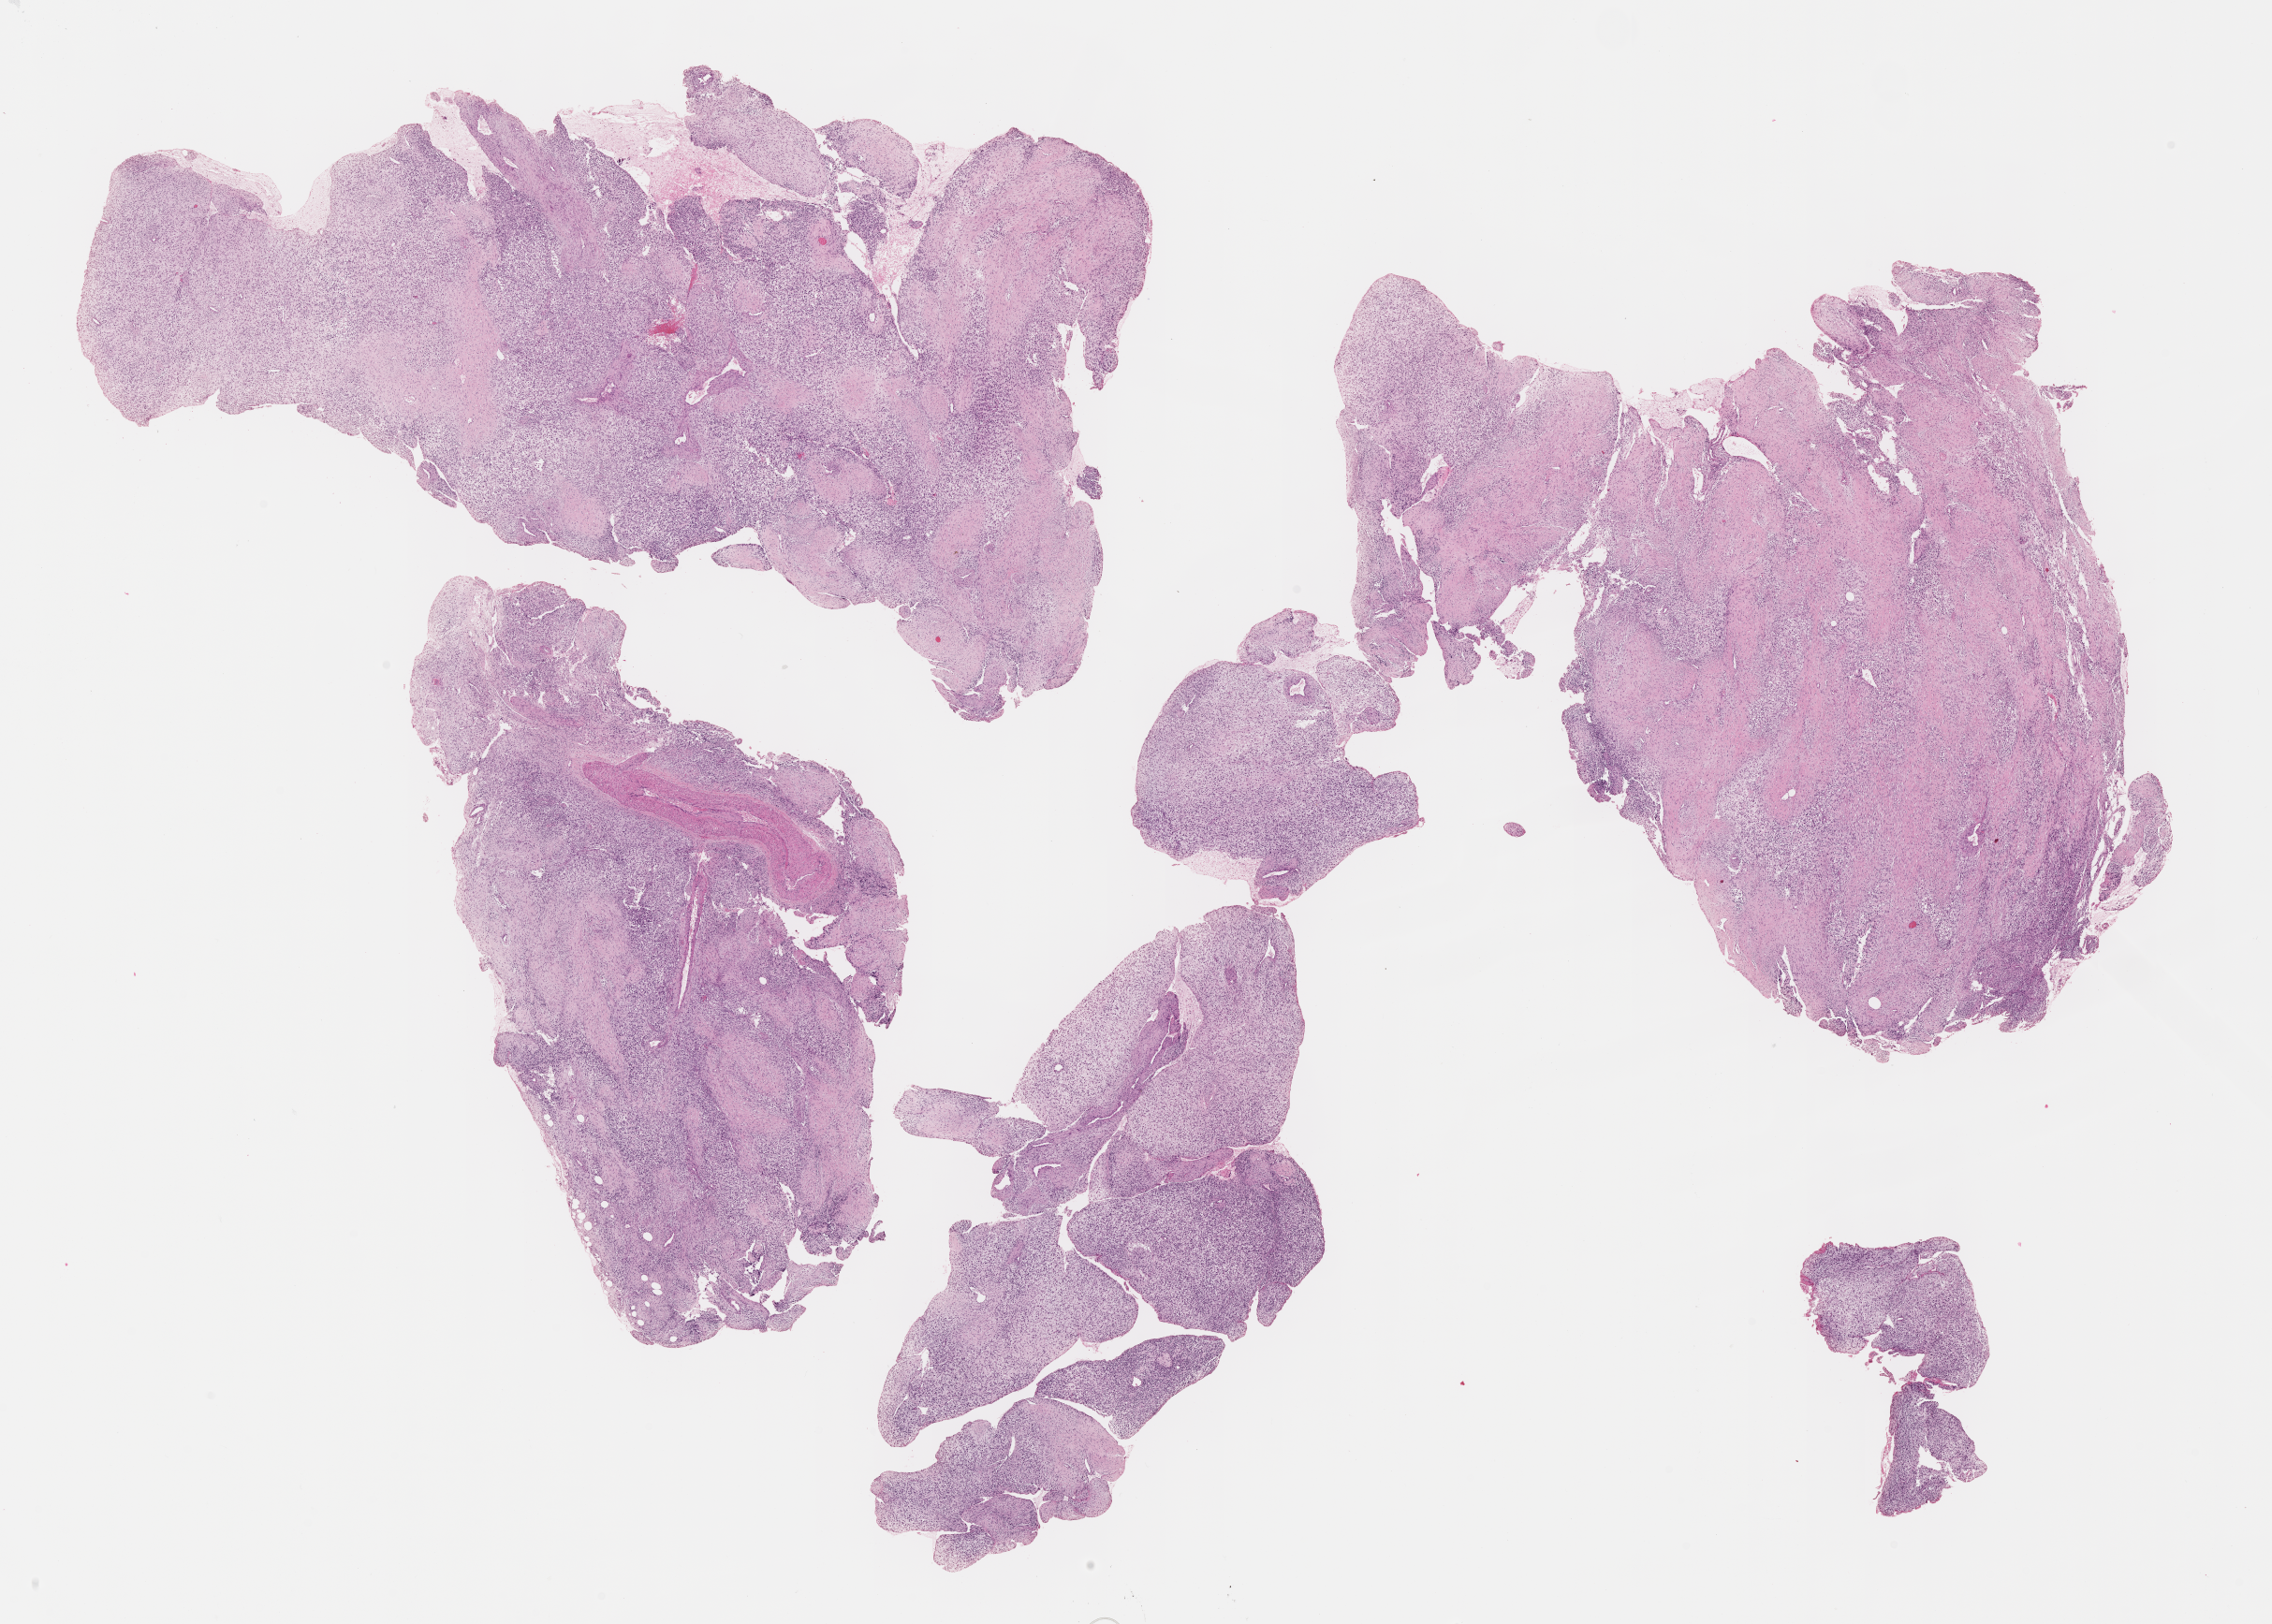
H&E whole-slide image of tumor tissue, whole scanned area (about 19.6 x 14.0 mm) shown as a low-resolution overview, formalin-fixed, paraffin-embedded (FFPE) tissue, site: bone, tibia. Male patient, age at diagnosis 7.1 years.
Primary site (case record): leg. Metastatic status at presentation (as recorded): non-metastatic. Stage (as recorded): 2. Diagnosis: rhabdomyosarcoma; histological classification: embryonal rhabdomyosarcoma.